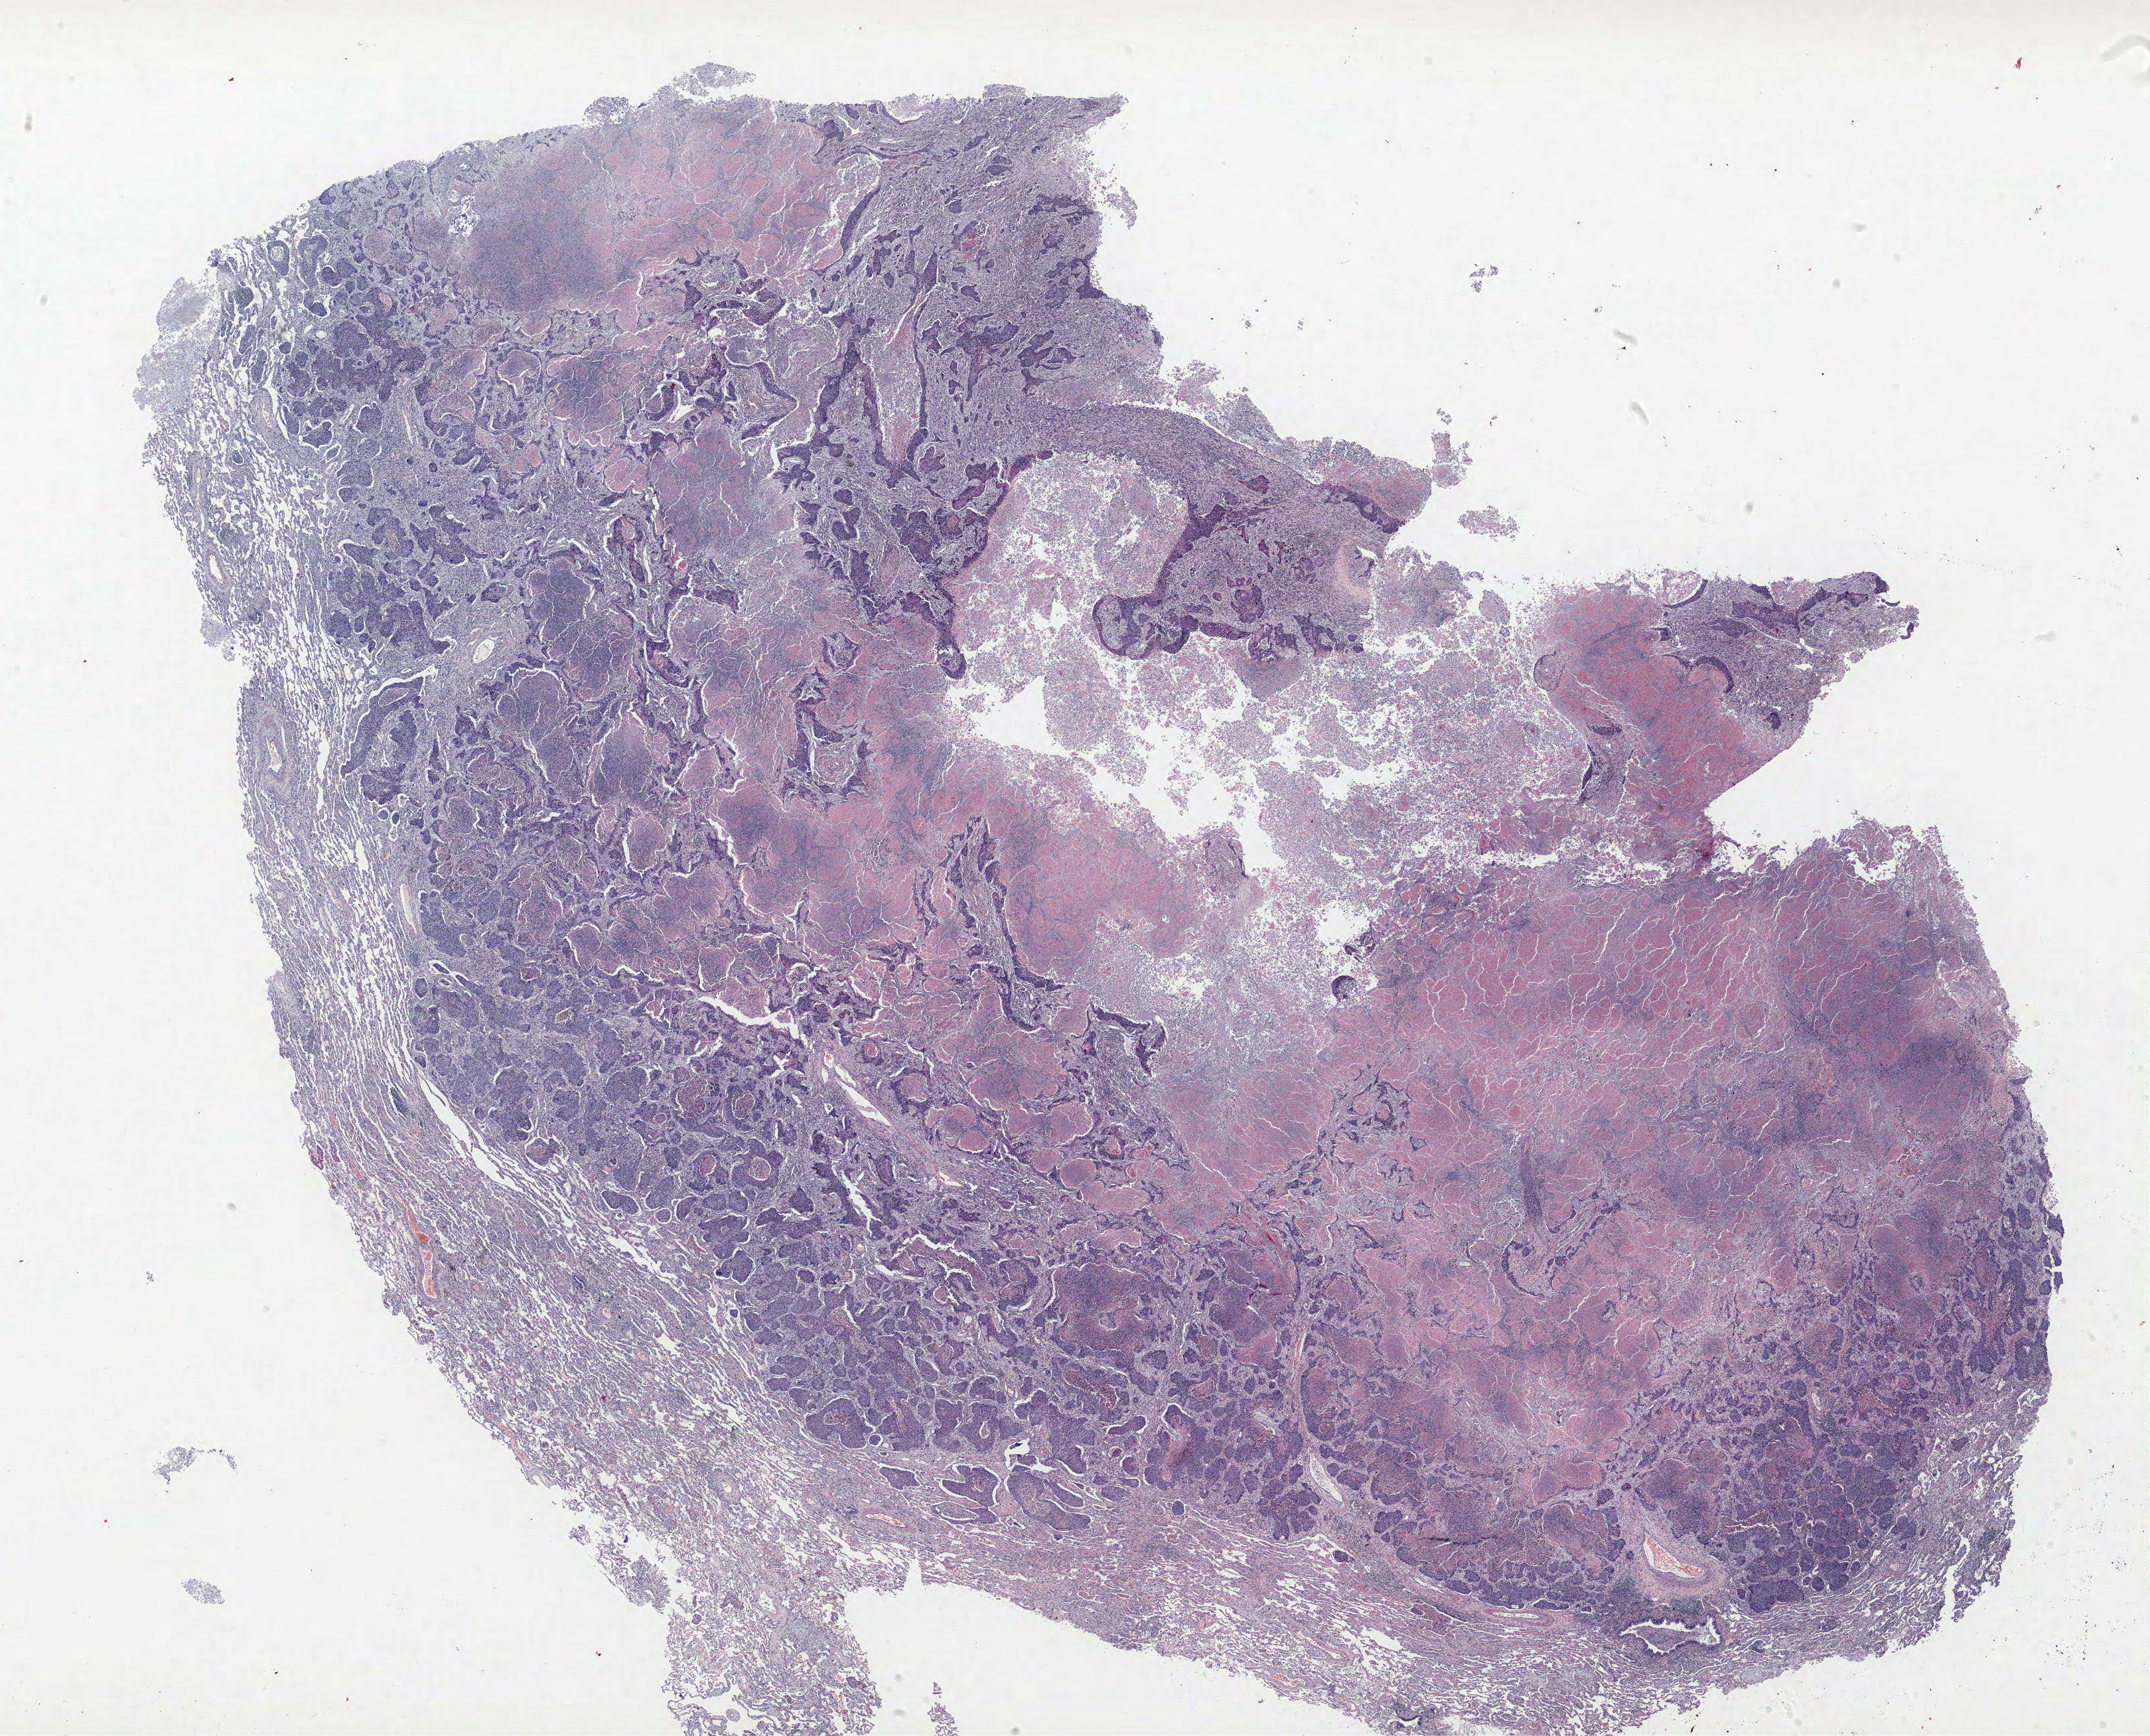
Hematoxylin and eosin (H&E) stained whole-slide image, low-resolution overview of the scanned area, about 25.9 x 20.9 mm (acquisition: 40x scan). Formalin-fixed paraffin-embedded (FFPE) section. Lung. Male, age 68 at enrolment. Grade: moderately differentiated (G2).
• participant's lung-cancer diagnosis: Adenosquamous carcinoma (ICD-O-3 8560/3)
• stage (AJCC 6th edition): IB
• tumour size (pathology): 40 mm
• primary tumour location (clinical record): right lower lobe